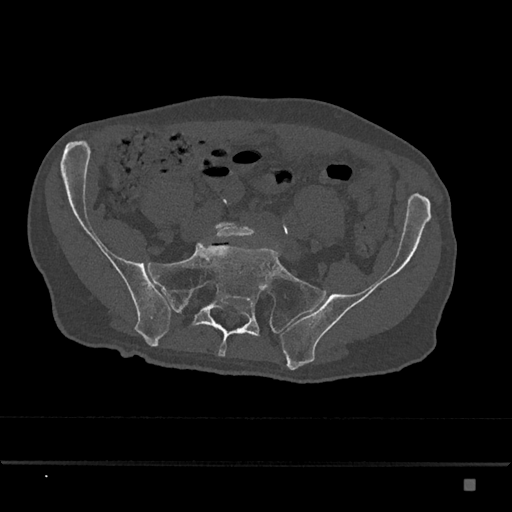
CT including the spine, one axial slice; position 210 of 797 along the scan axis; reconstruction kernel Br40s/3; 120 kVp; bone window (W 1800 / L 400 HU); 0.5 mm slice thickness; 512 × 512 image matrix, field of view 390 × 390 mm. Patient: male, 72 years. From the clinical record (not read from this slice): primary cancer: prostate.
Annotated regions visible in this slice (semi-automatically segmented with operator editing):
- L5 vertebra: box from (x=214, y=222) to (x=256, y=240) px